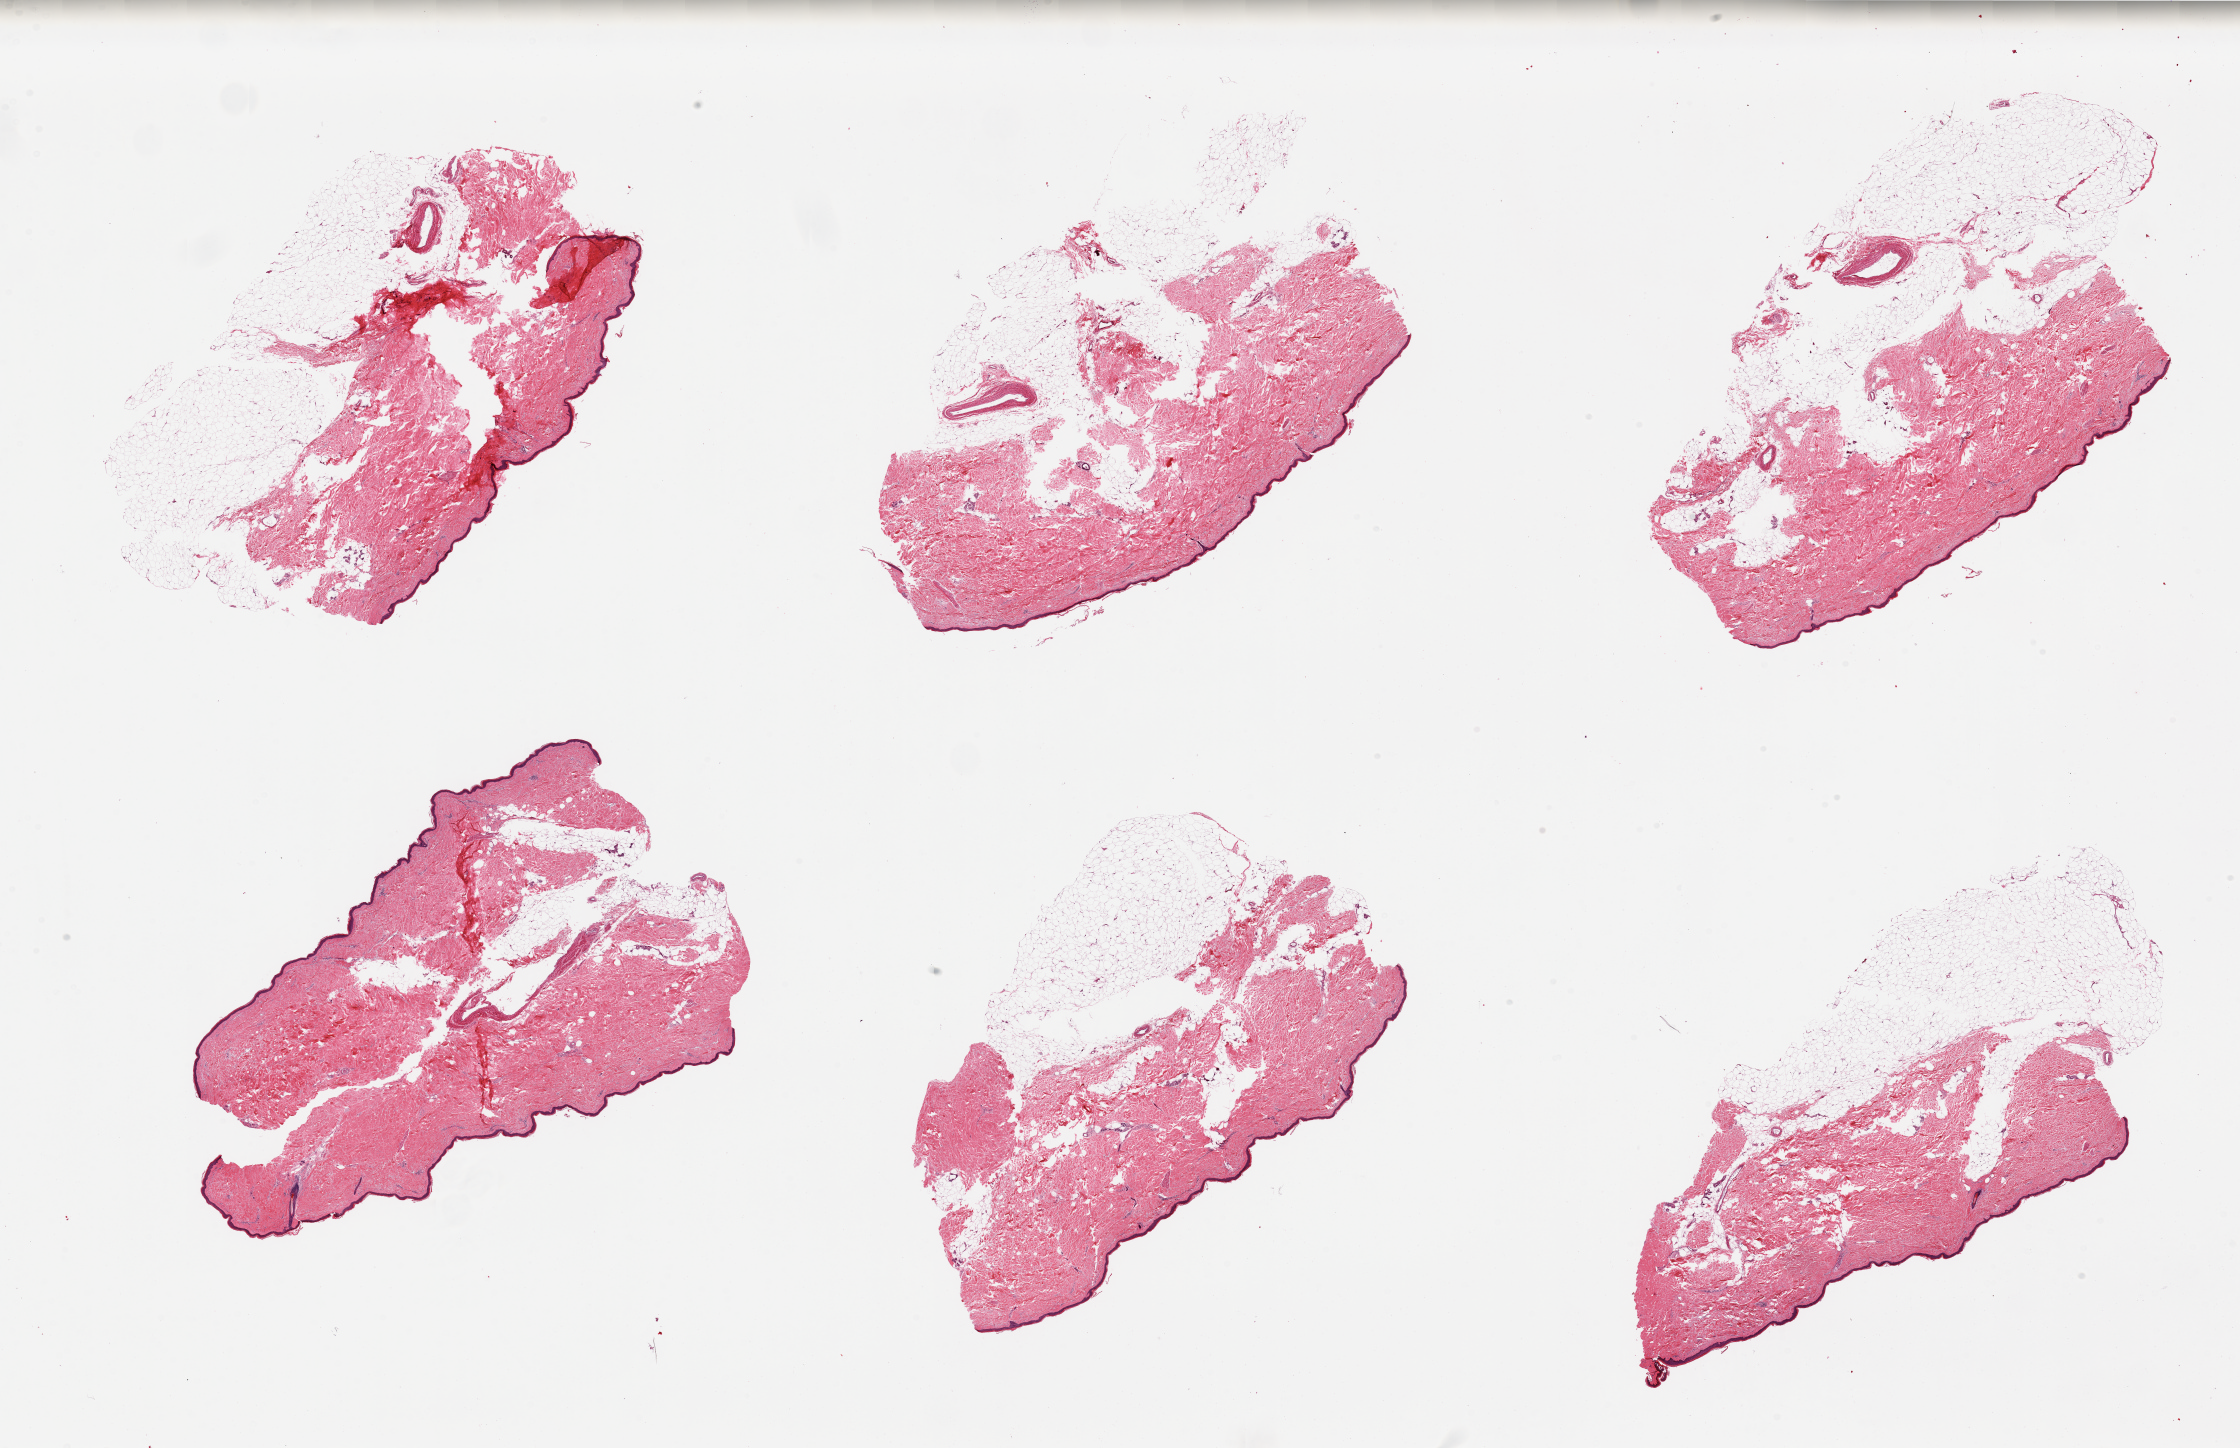
Digitized haematoxylin and eosin-stained section, shown as a low-resolution overview of the whole scanned area (about 35.4 x 22.9 mm). PAXgene-fixed paraffin-embedded (PFPE) section. Target tissue: skin of lower leg. Tissue donor sample. Donor: female.
Pathologist's review note for this sample: 6 pieces; Prominent adherent dermal fat on 4/6 up to ~2.5mm thick.